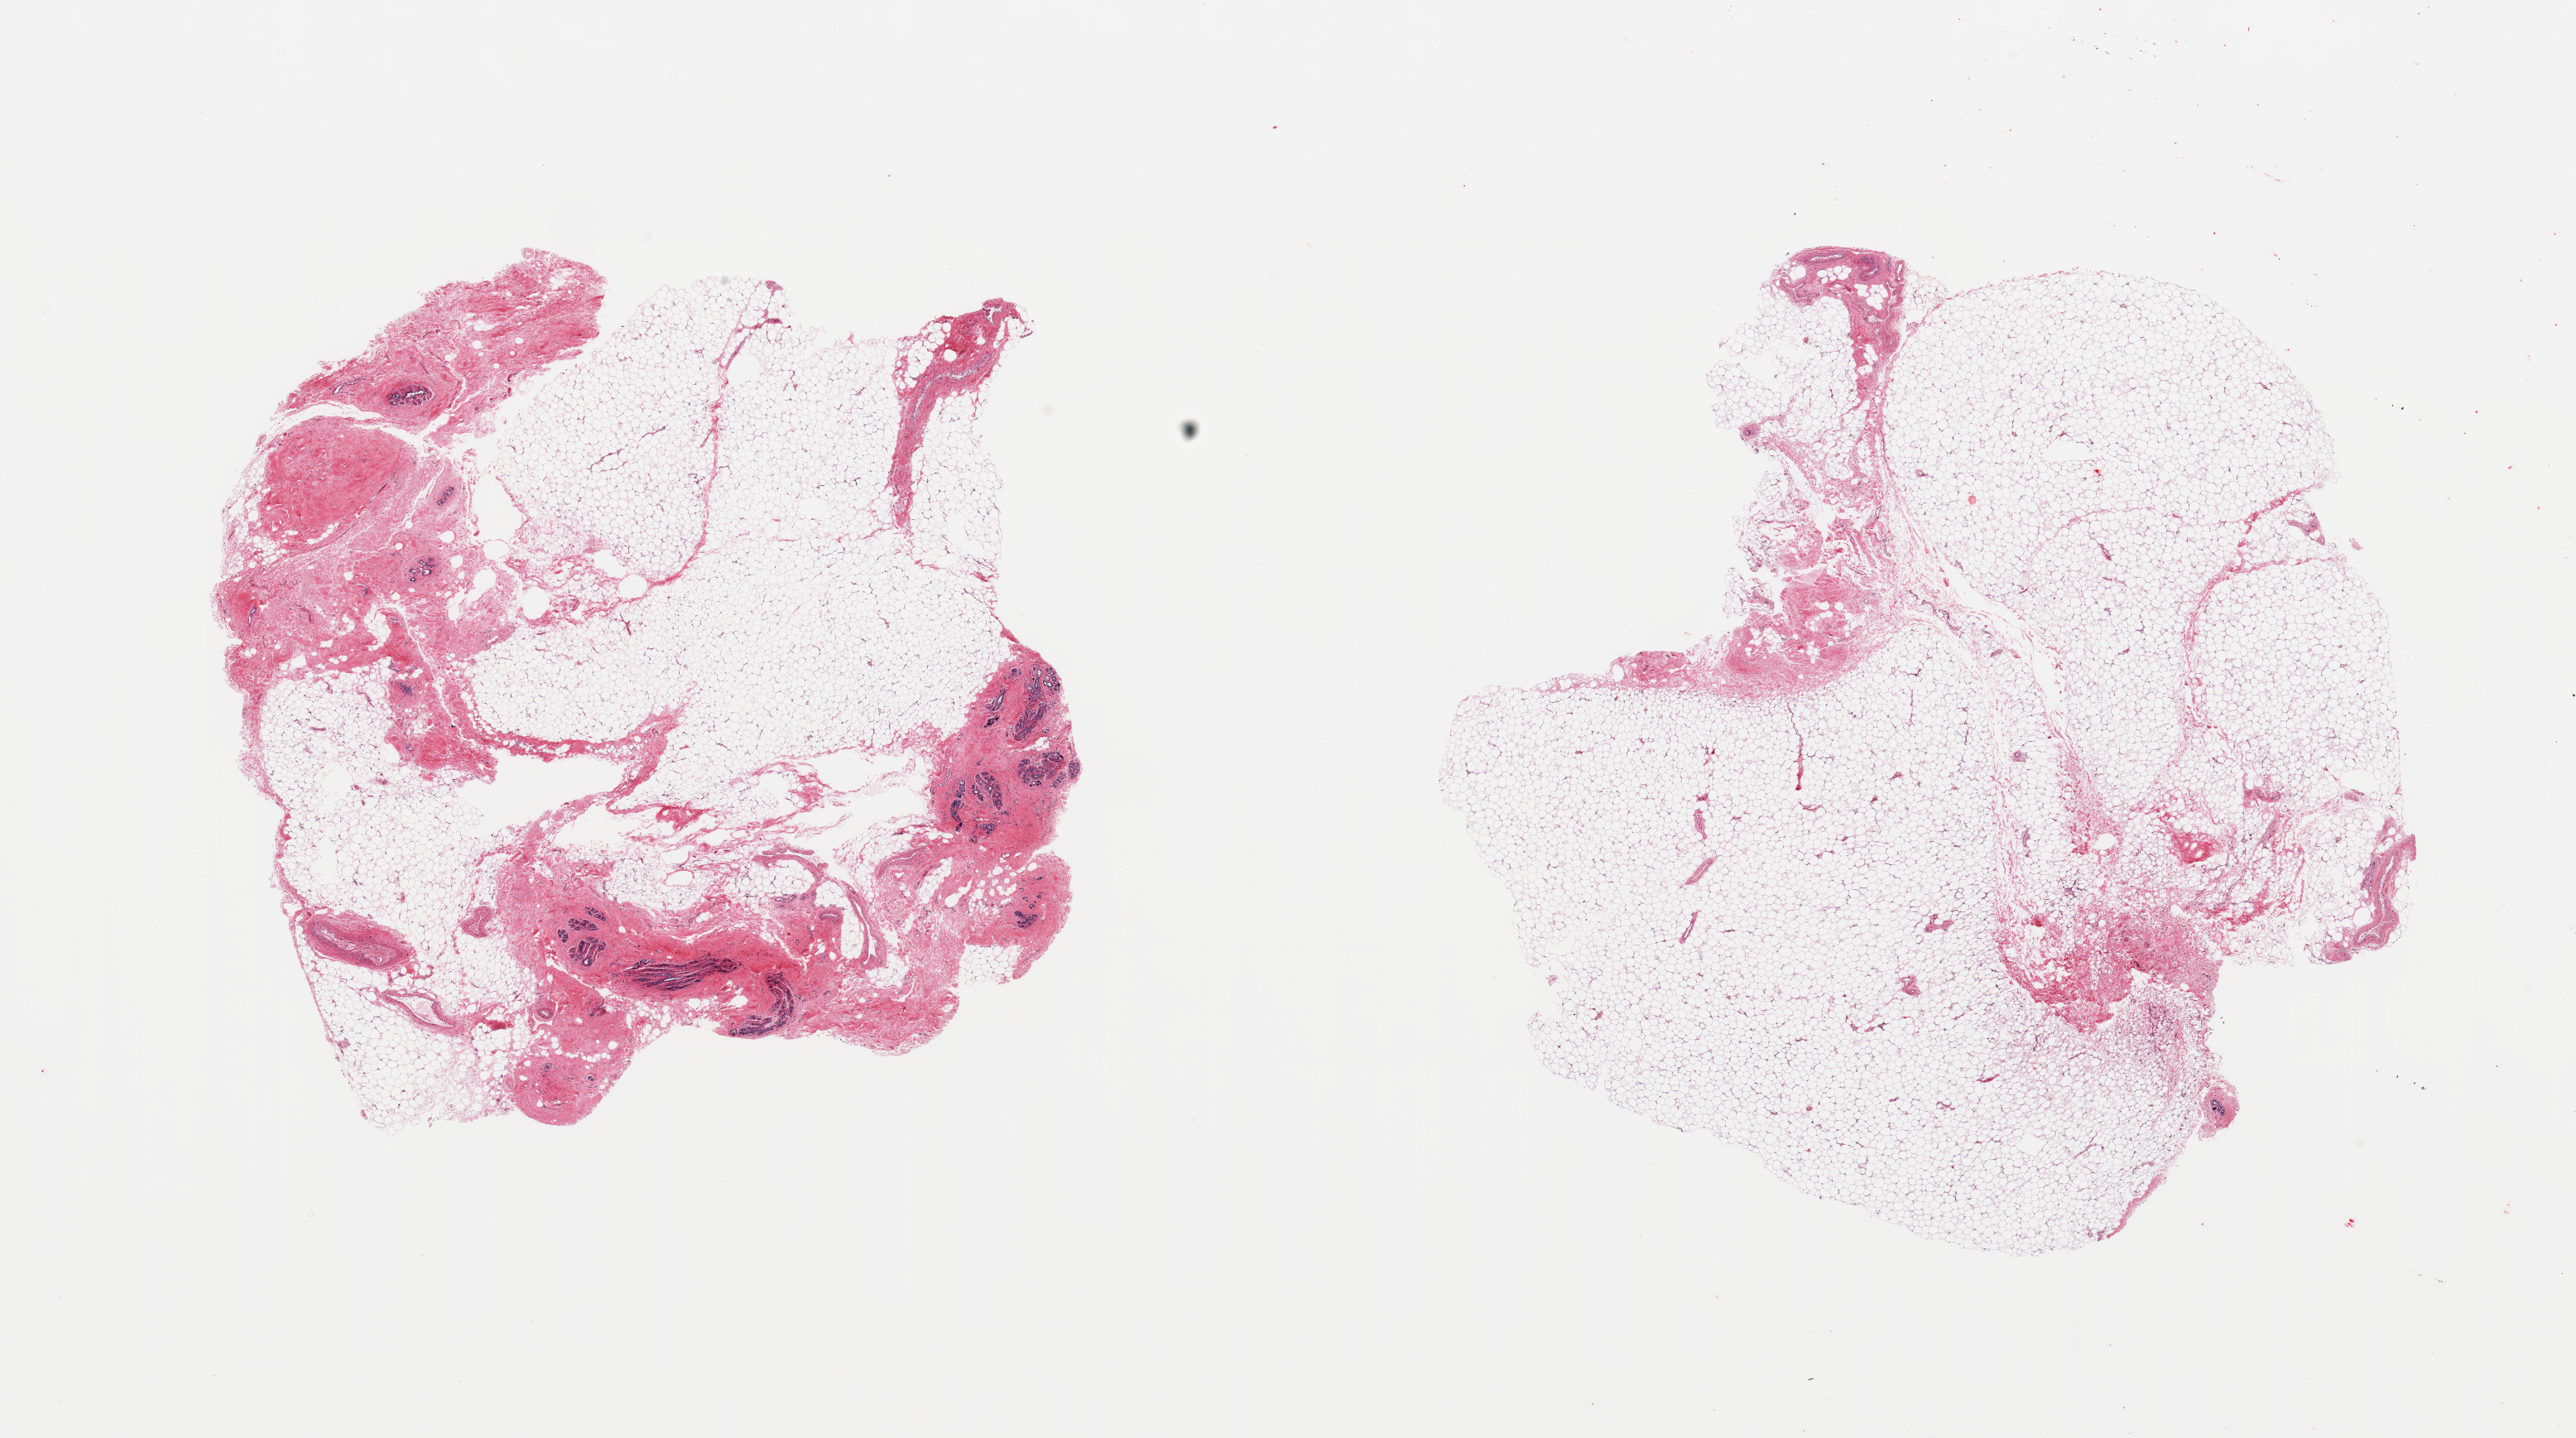
Haematoxylin and eosin whole-slide image, brightfield, low-resolution overview of the scanned area, about 24.6 x 13.7 mm (slide scanned at 20x); PAXgene-fixed paraffin-embedded (PFPE) section; target tissue: breast; tissue donor sample. Donor sex: female.
Pathologist's review note for this sample: 2 pieces; smooth muscle proliferation around ducts & lobules (fibrous mastopathy) in 1 piece with 80% fat; lobular microcalcifications; other piece is without mammary tissue, with 90% fat.